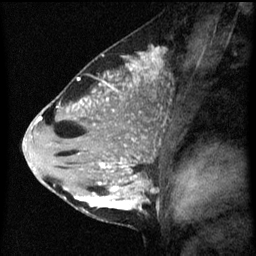
Breast MRI (dynamic contrast-enhanced), one sagittal slice; dynamic contrast-enhanced series, image 2 of 3 at this slice position (ordered by acquisition); 1.5 T; TE 4.2 ms, TR 8 ms; 256 × 256 image matrix, field of view 180 × 180 mm. Female patient, age 33 years.
Annotated regions visible in this slice (semi-automatic segmentation, software-assisted and operator-edited):
- analysis volume of interest (the breast-tissue region the enhancement analysis was run in; not a lesion): bounding box (x1, y1, x2, y2) in pixels: (71, 118, 161, 215)
- tumour enhancement mask (voxels above the 70 % enhancement threshold inside the analysis volume of interest): (74, 162, 142, 211)